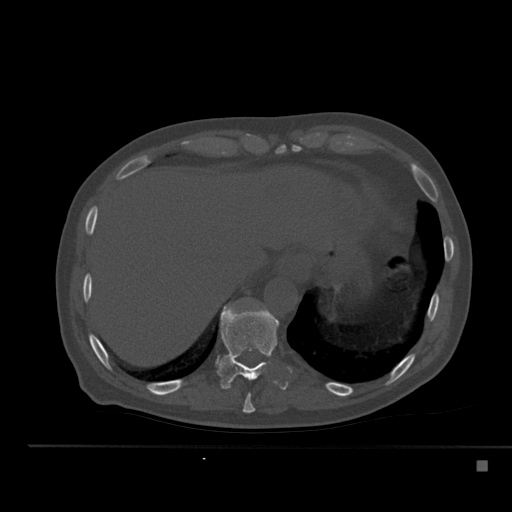
CT including the spine, one axial slice; position 269 of 517 along the scan axis; reconstruction kernel Br40s; bone window (W 1800 / L 400 HU); 512 × 512 image matrix. Male patient, age 70 years. Case-level facts recorded for this patient, not image findings: primary cancer: renal; vertebrae with lytic lesions (as recorded): T4, T6, T10, T12, L3, L4, L5.
Outlined on this slice (semi-automatic segmentation, software-assisted and operator-edited):
- T10 vertebra: bounding box <217,307,279,389> (left, top, right, bottom; pixels)
- T9 vertebra: <242,393,255,413>